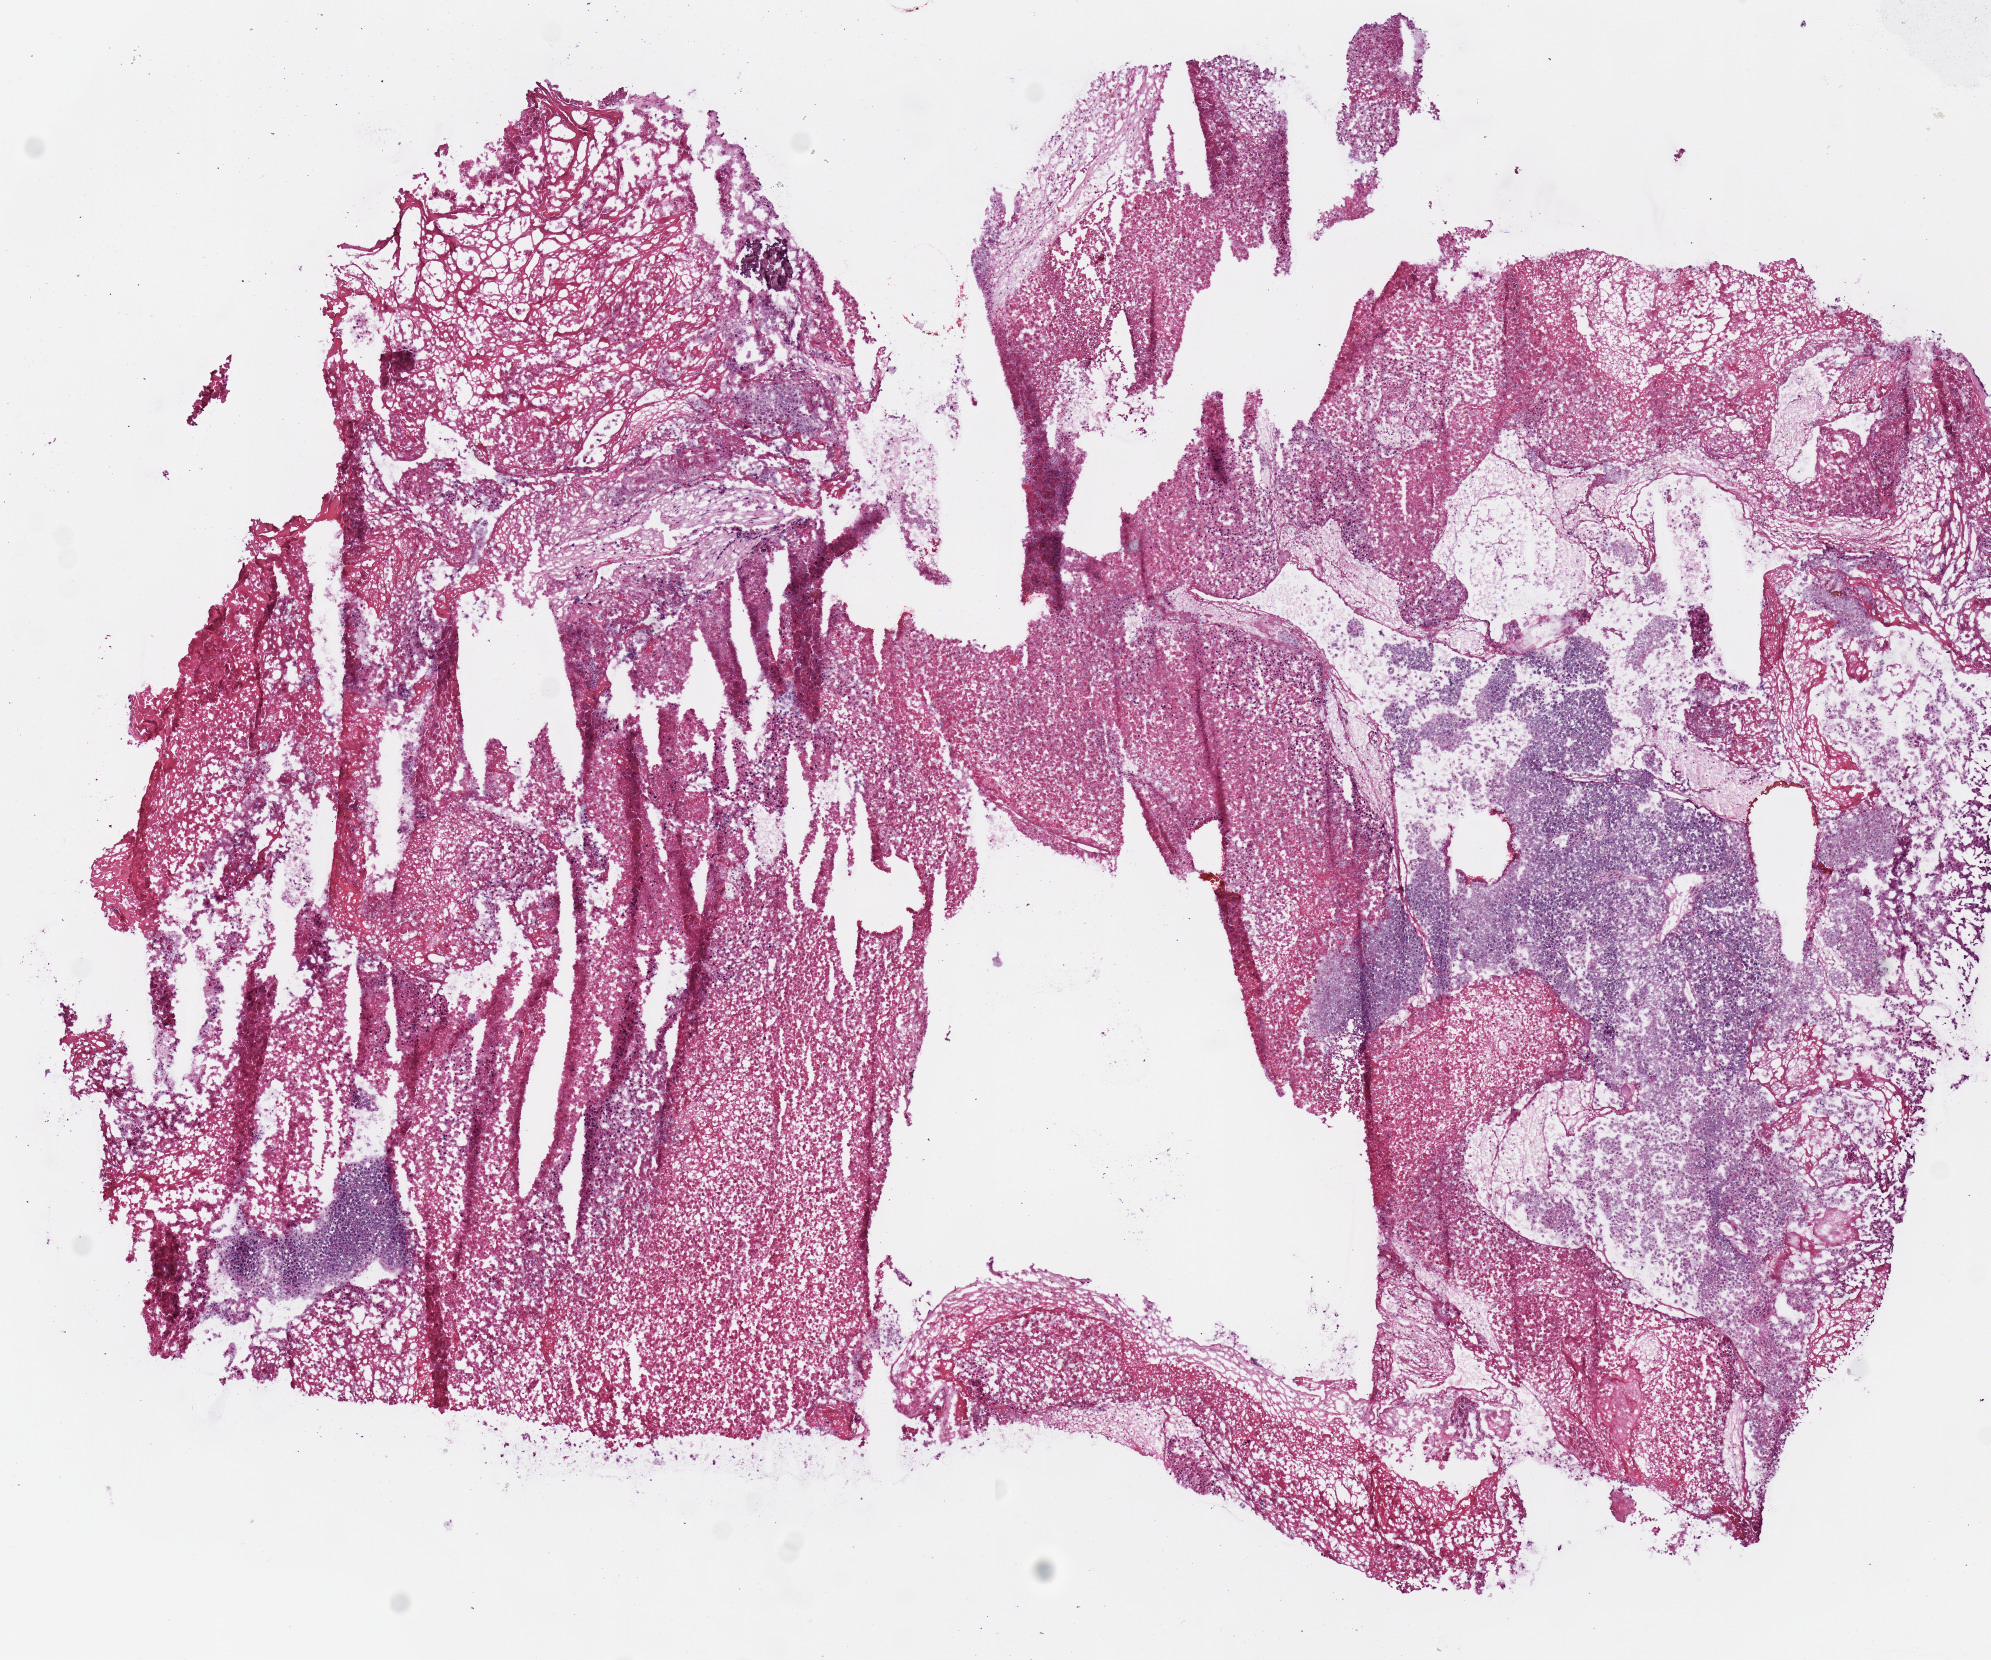
Digitized H&E tissue section (whole slide), a low-resolution overview of the entire scanned area, about 7.9 x 6.6 mm (acquisition: 20x scan). Frozen section. Sample: primary tumour, bladder. Male patient; age at initial diagnosis 79 years. Pathologist review of this section (percent, as recorded): tumour cells 100%, tumour nuclei 90%.
Pathologic diagnosis: Transitional cell carcinoma.